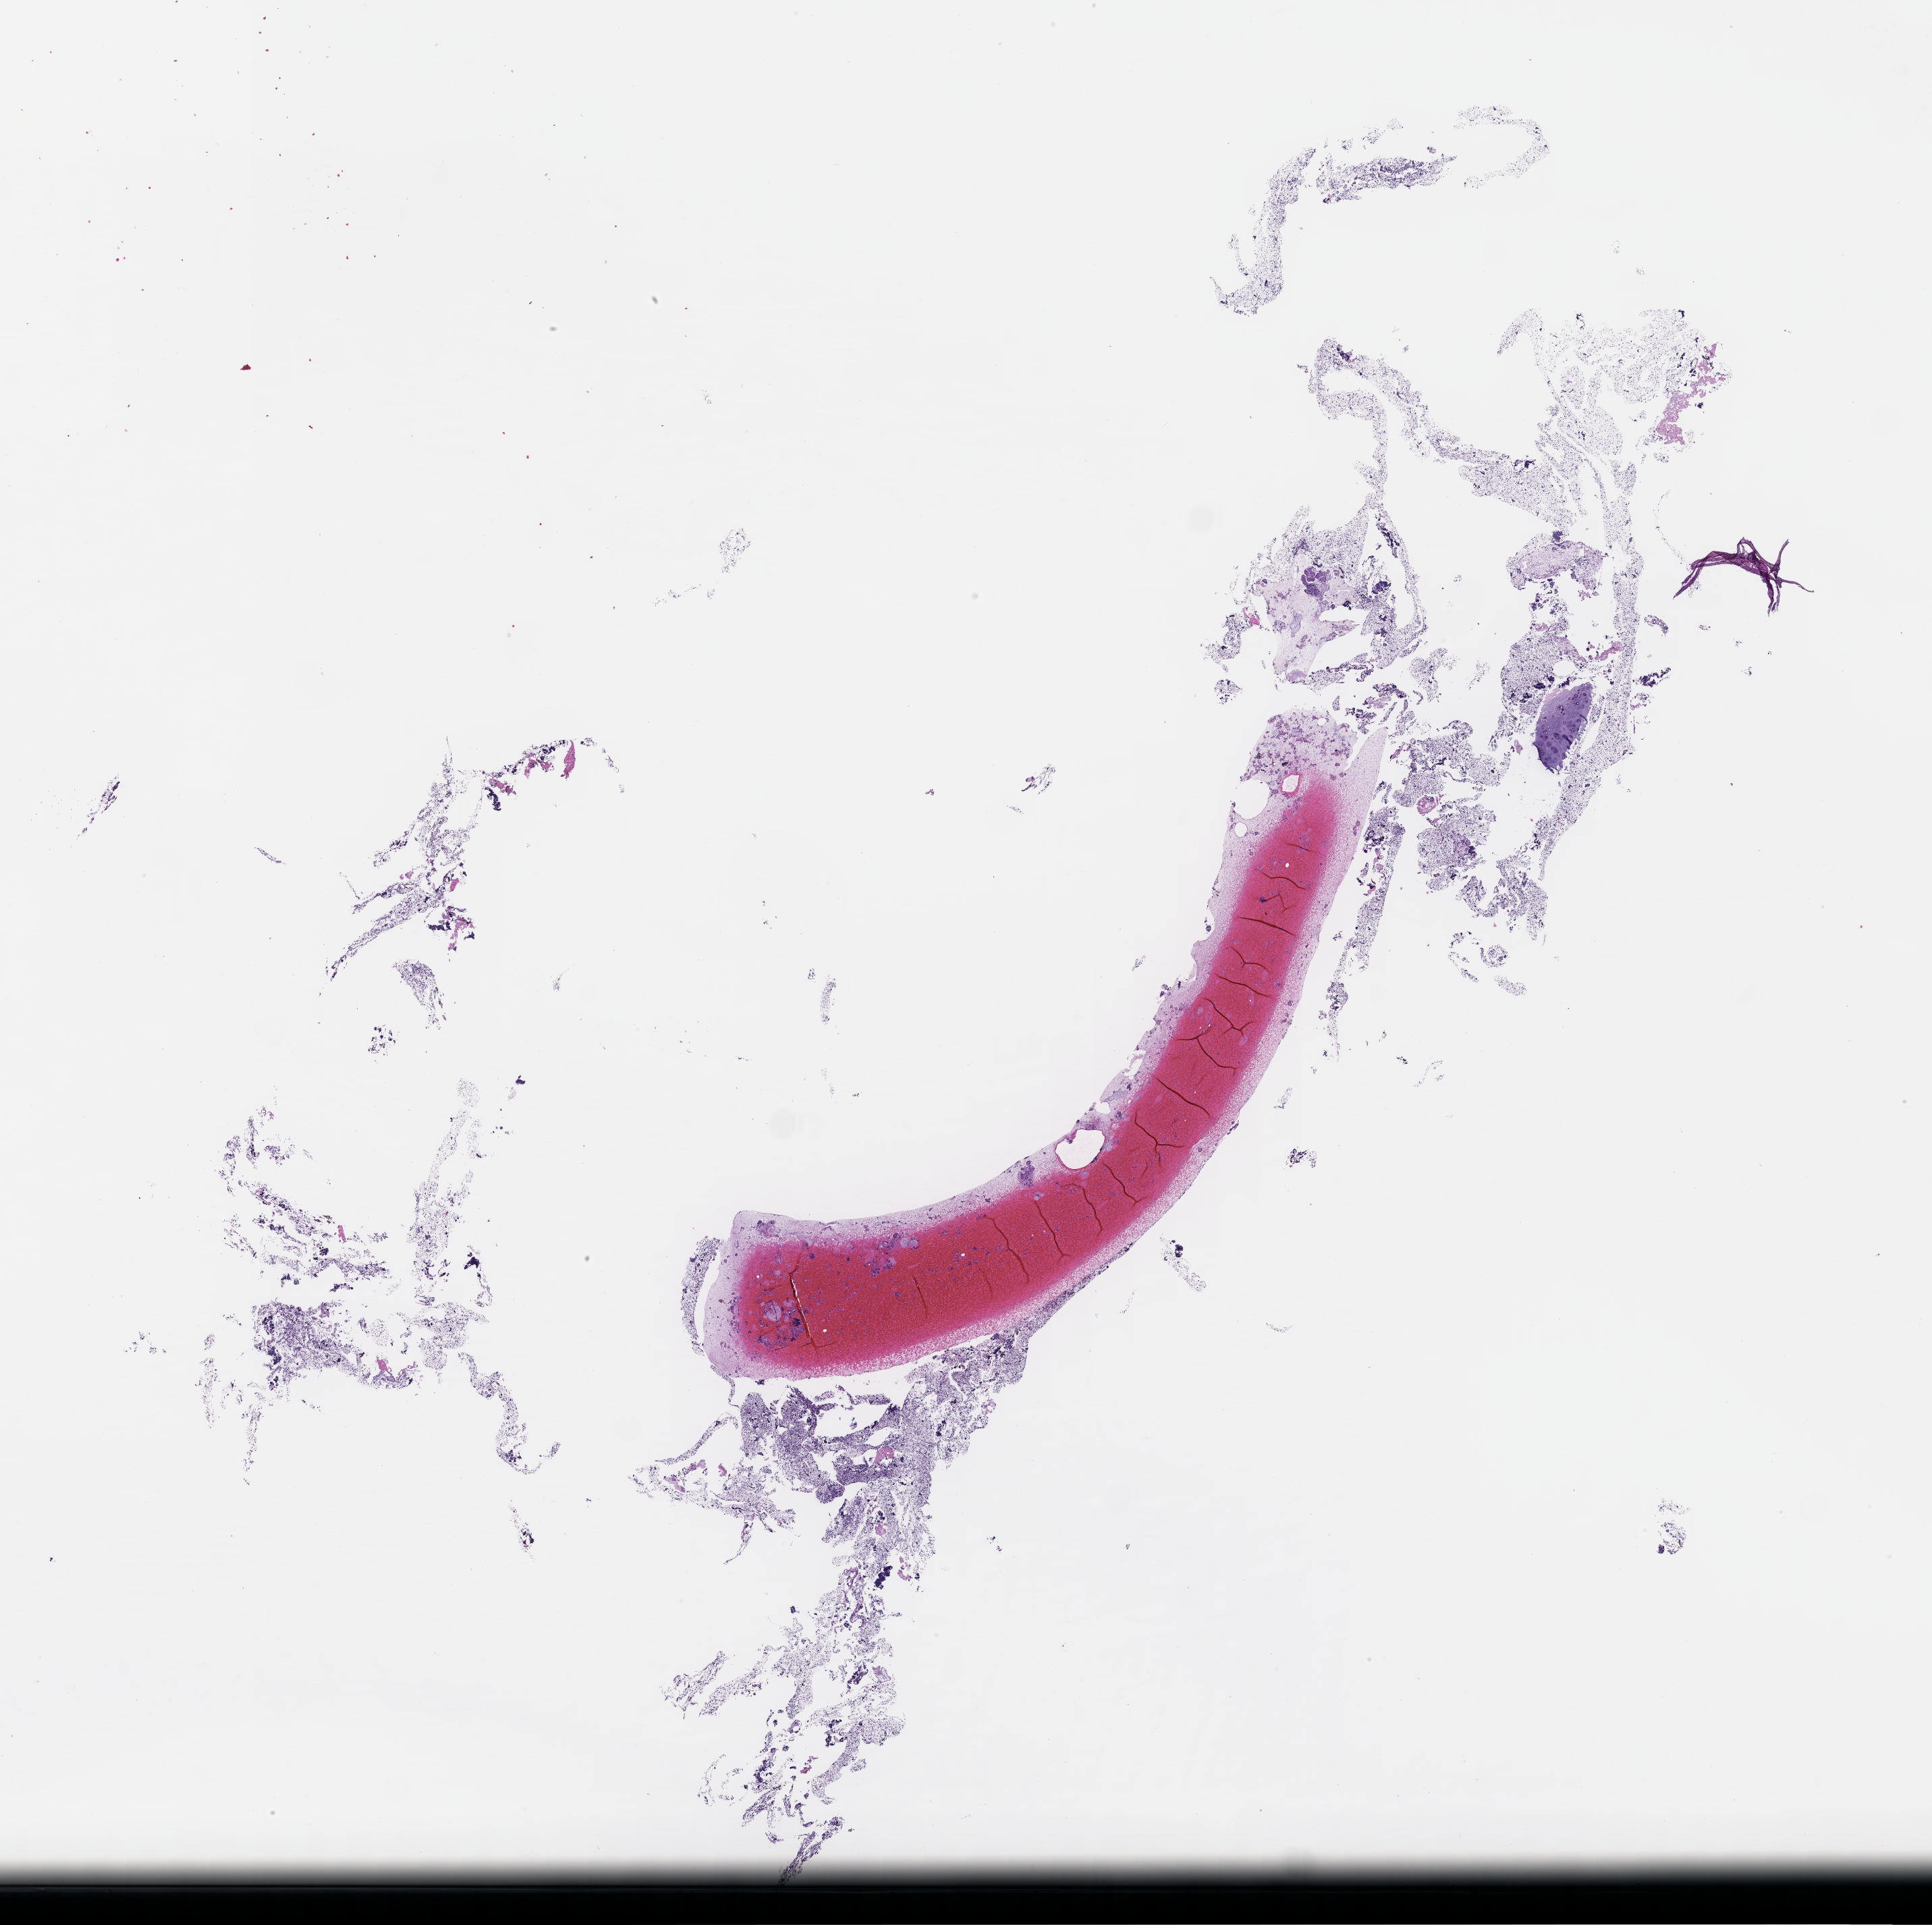
Whole-slide image, hematoxylin and eosin (H&E) stain, shown as a low-resolution overview of the whole scanned area (about 23.1 x 23.0 mm), formalin-fixed paraffin-embedded section, specimen time point: archival tissue. Female patient.
This section: metastatic tumor tissue. Patient diagnosis (primary): Small Cell Lung Carcinoma.